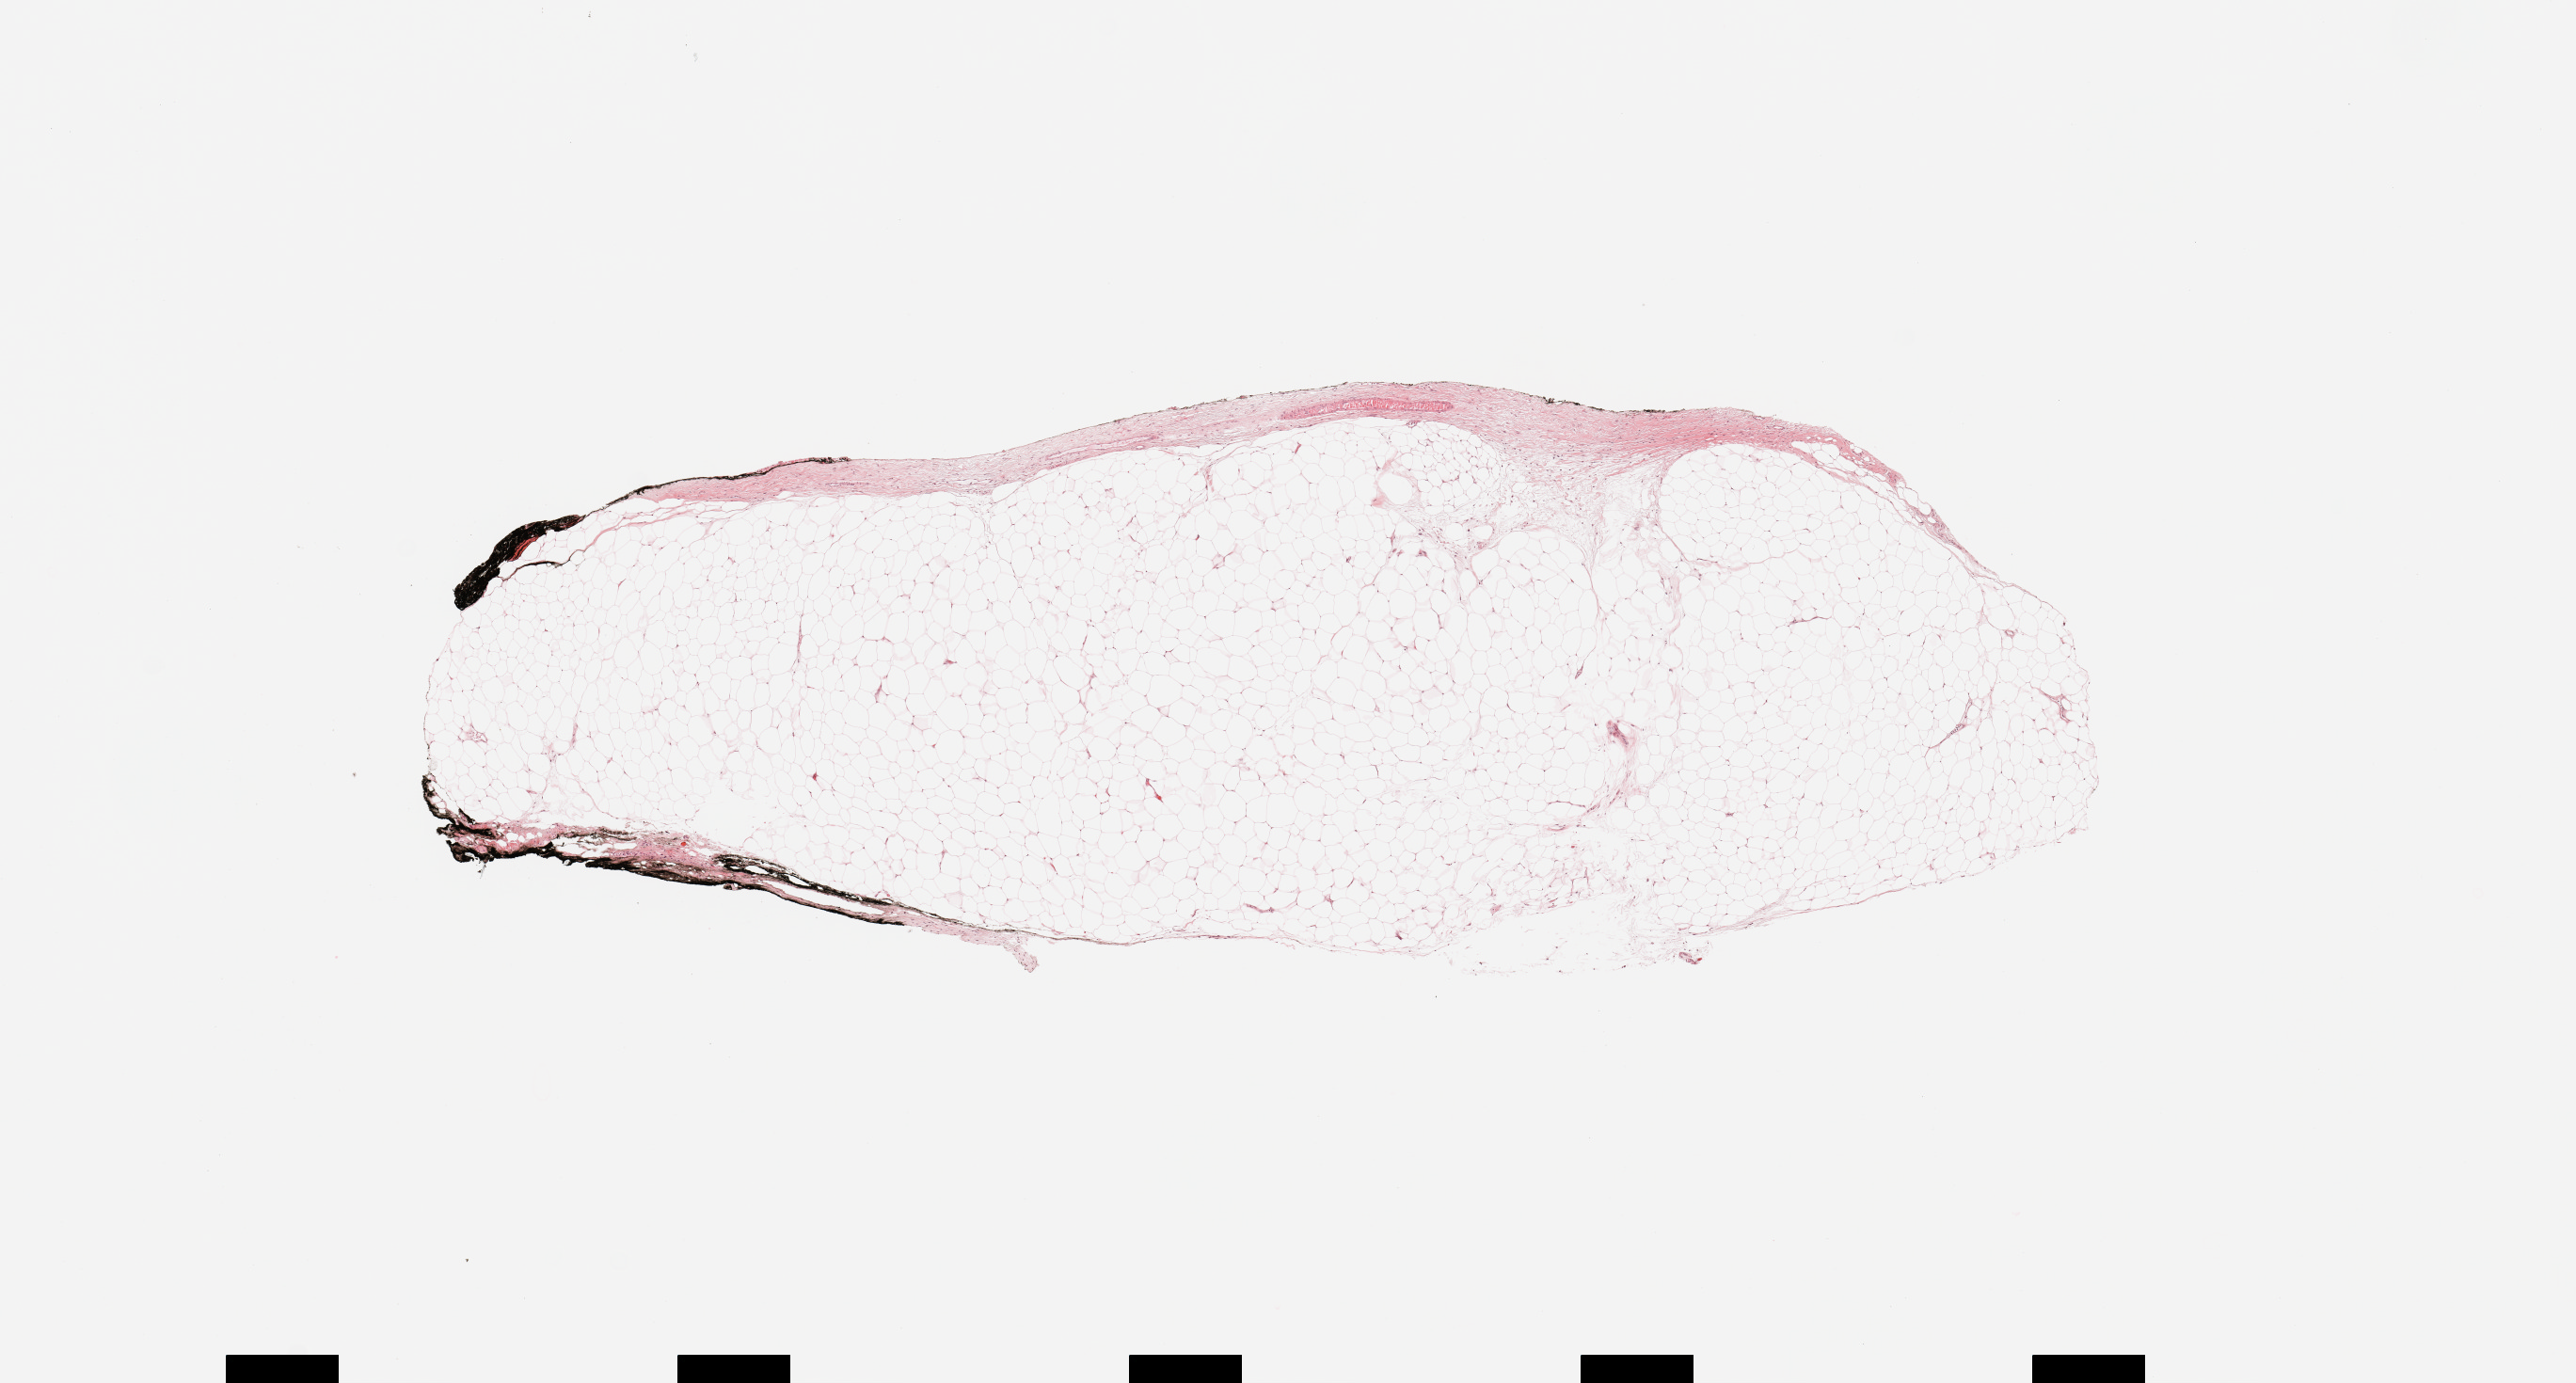
Digitized H&E-stained tissue section (whole slide) — whole scanned area (about 10.8 x 5.8 mm, slide scanned at 20x) shown as a low-resolution overview; normal (non-tumour) tissue sample, kidney. Patient: male, age 59 years.
This section: normal (non-tumour) tissue from the same patient. Patient diagnosis: Renal cell carcinoma, NOS.